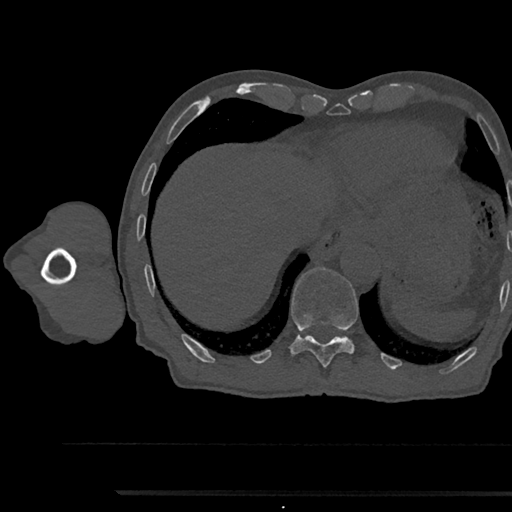
CT including the spine, one axial slice. Slice 783 of 797 in the series (ordered by position). Reconstruction kernel Br40s/3. Bone window (W 1800 / L 400 HU). 0.5 mm slice thickness. 512 × 512 image matrix. Patient: male, 79 years. Case-level facts recorded for this patient, not image findings: primary cancer: prostate.
Annotated regions visible in this slice (semi-automatically segmented with operator editing):
- T11 vertebra: bounding box [x1, y1, x2, y2] px = [291, 267, 359, 368]